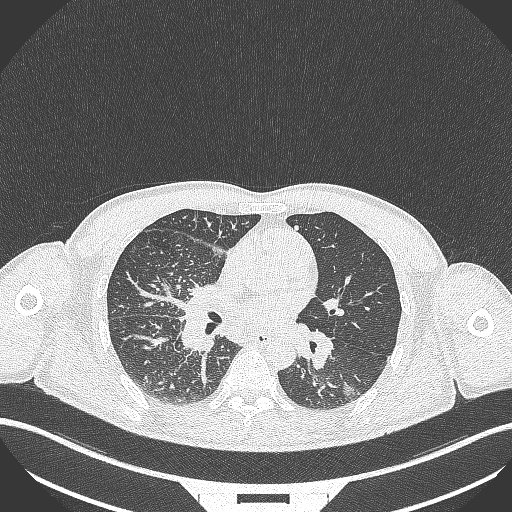
Chest CT, one axial slice; 120 kVp; lung window (W 1500 / L -600 HU); 512 × 512 image matrix, field of view 400 × 400 mm. Male patient, age 49 years. Case-level facts recorded for this patient, not image findings: clinical TNM (as recorded): T2b N1 M0.
Outlined on this slice (bounding box drawn by a radiologist):
- lung tumour (recorded histology: adenocarcinoma): bounding box [x1, y1, x2, y2] px = [340, 377, 360, 403]